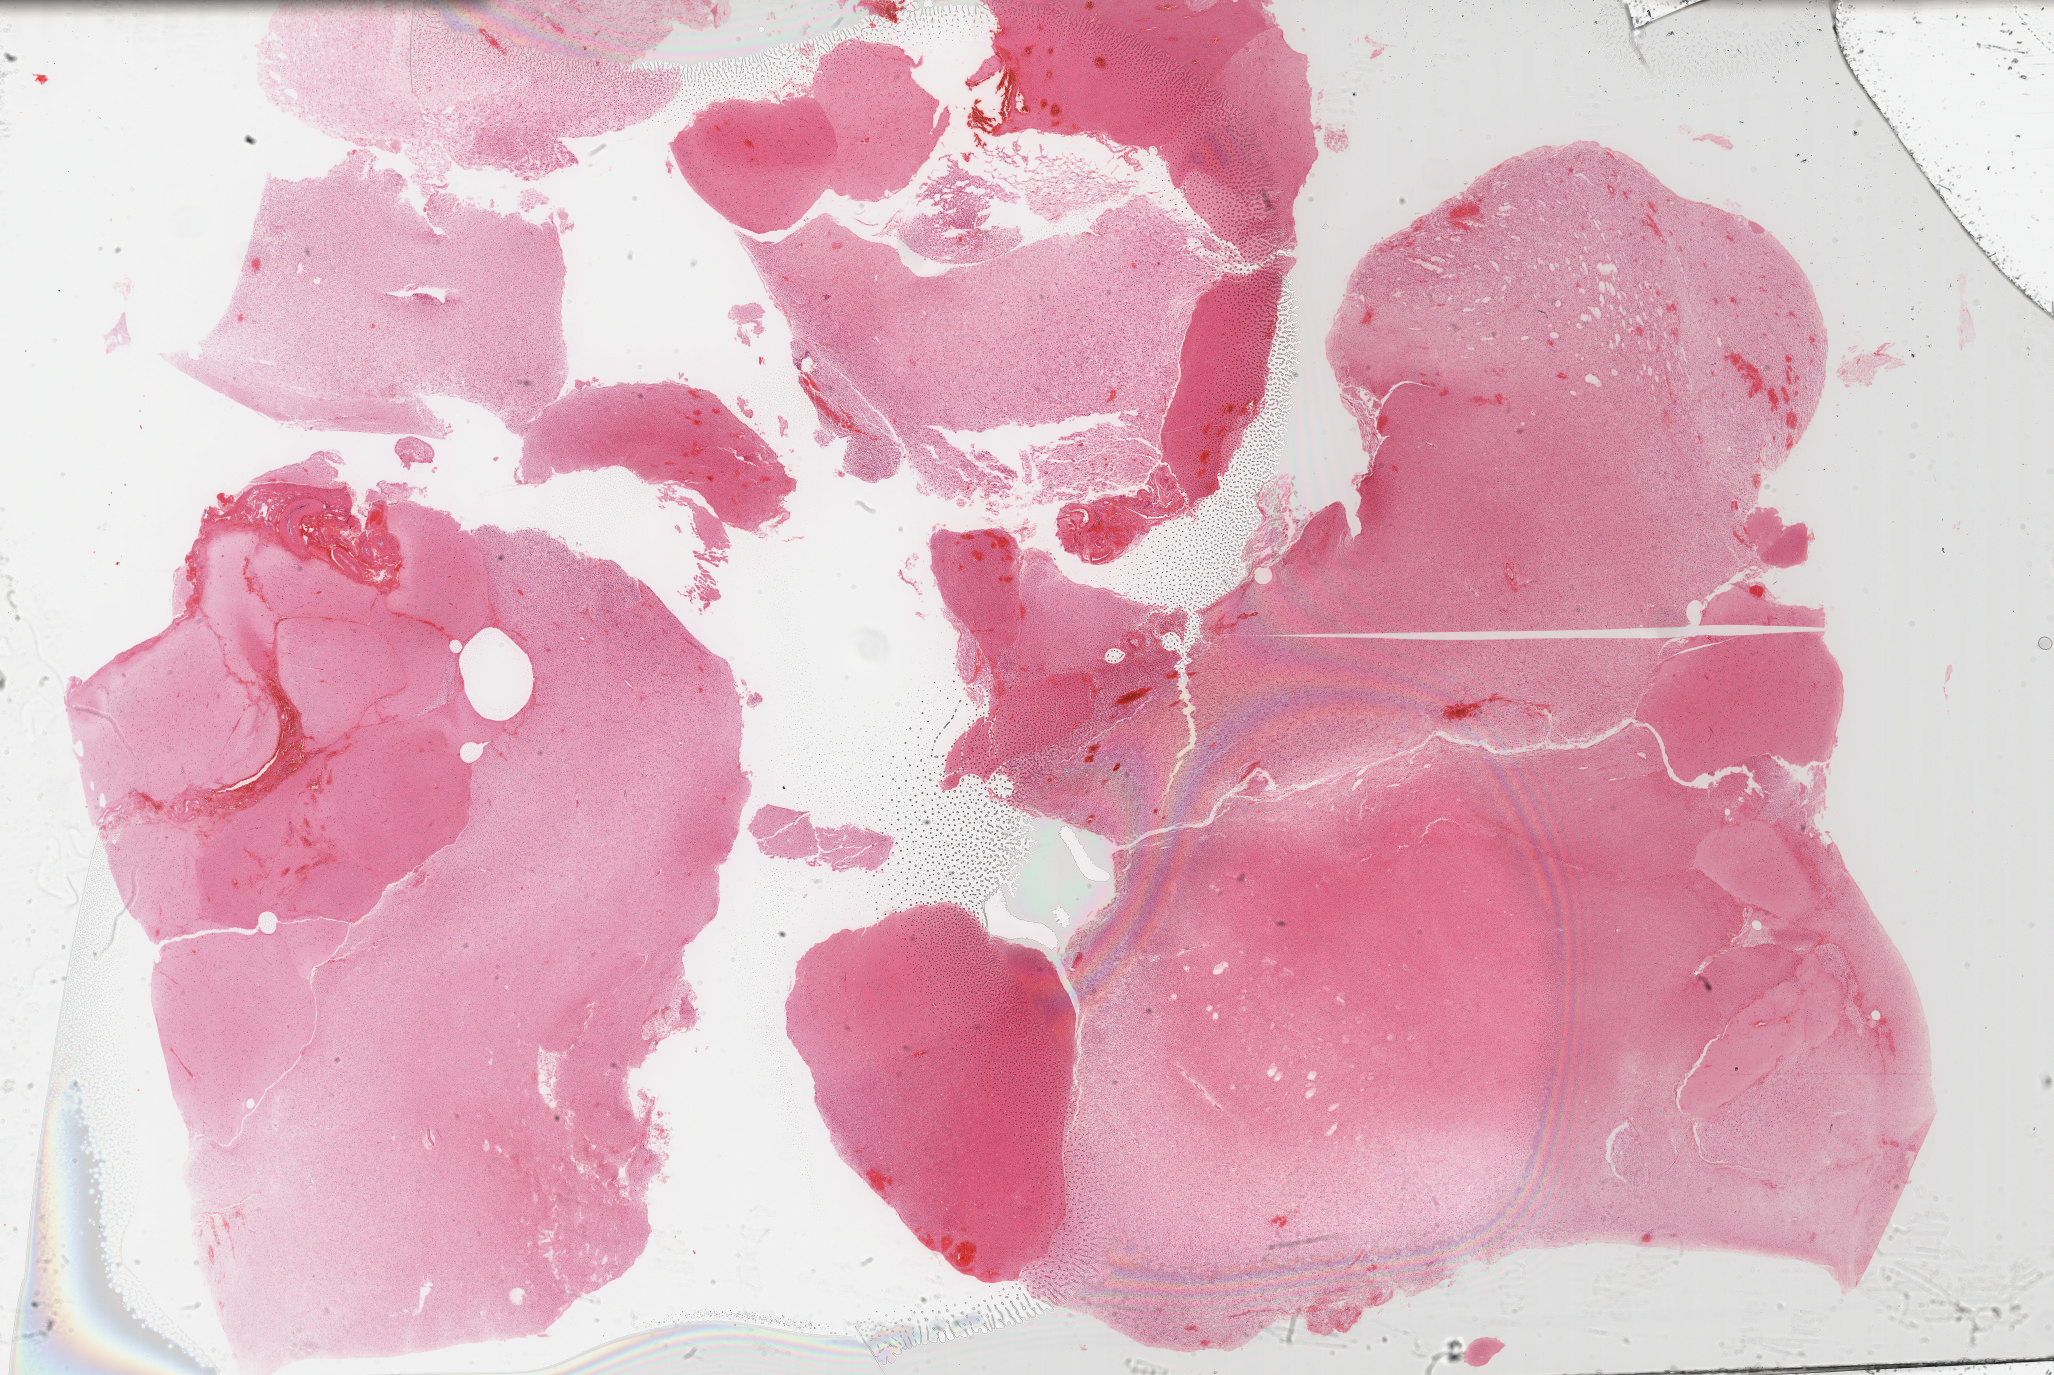
Hematoxylin and eosin (H&E) stained whole-slide image, low-resolution overview of the scanned area, about 33.2 x 22.2 mm (acquisition: 40x scan). Formalin-fixed paraffin-embedded (FFPE) diagnostic section. Brain, primary tumour sample. Patient: female, age at initial diagnosis 28 years. Histologic grade: G2 (moderately differentiated).
- pathologic diagnosis: Astrocytoma, NOS (cerebrum)
- laterality: left